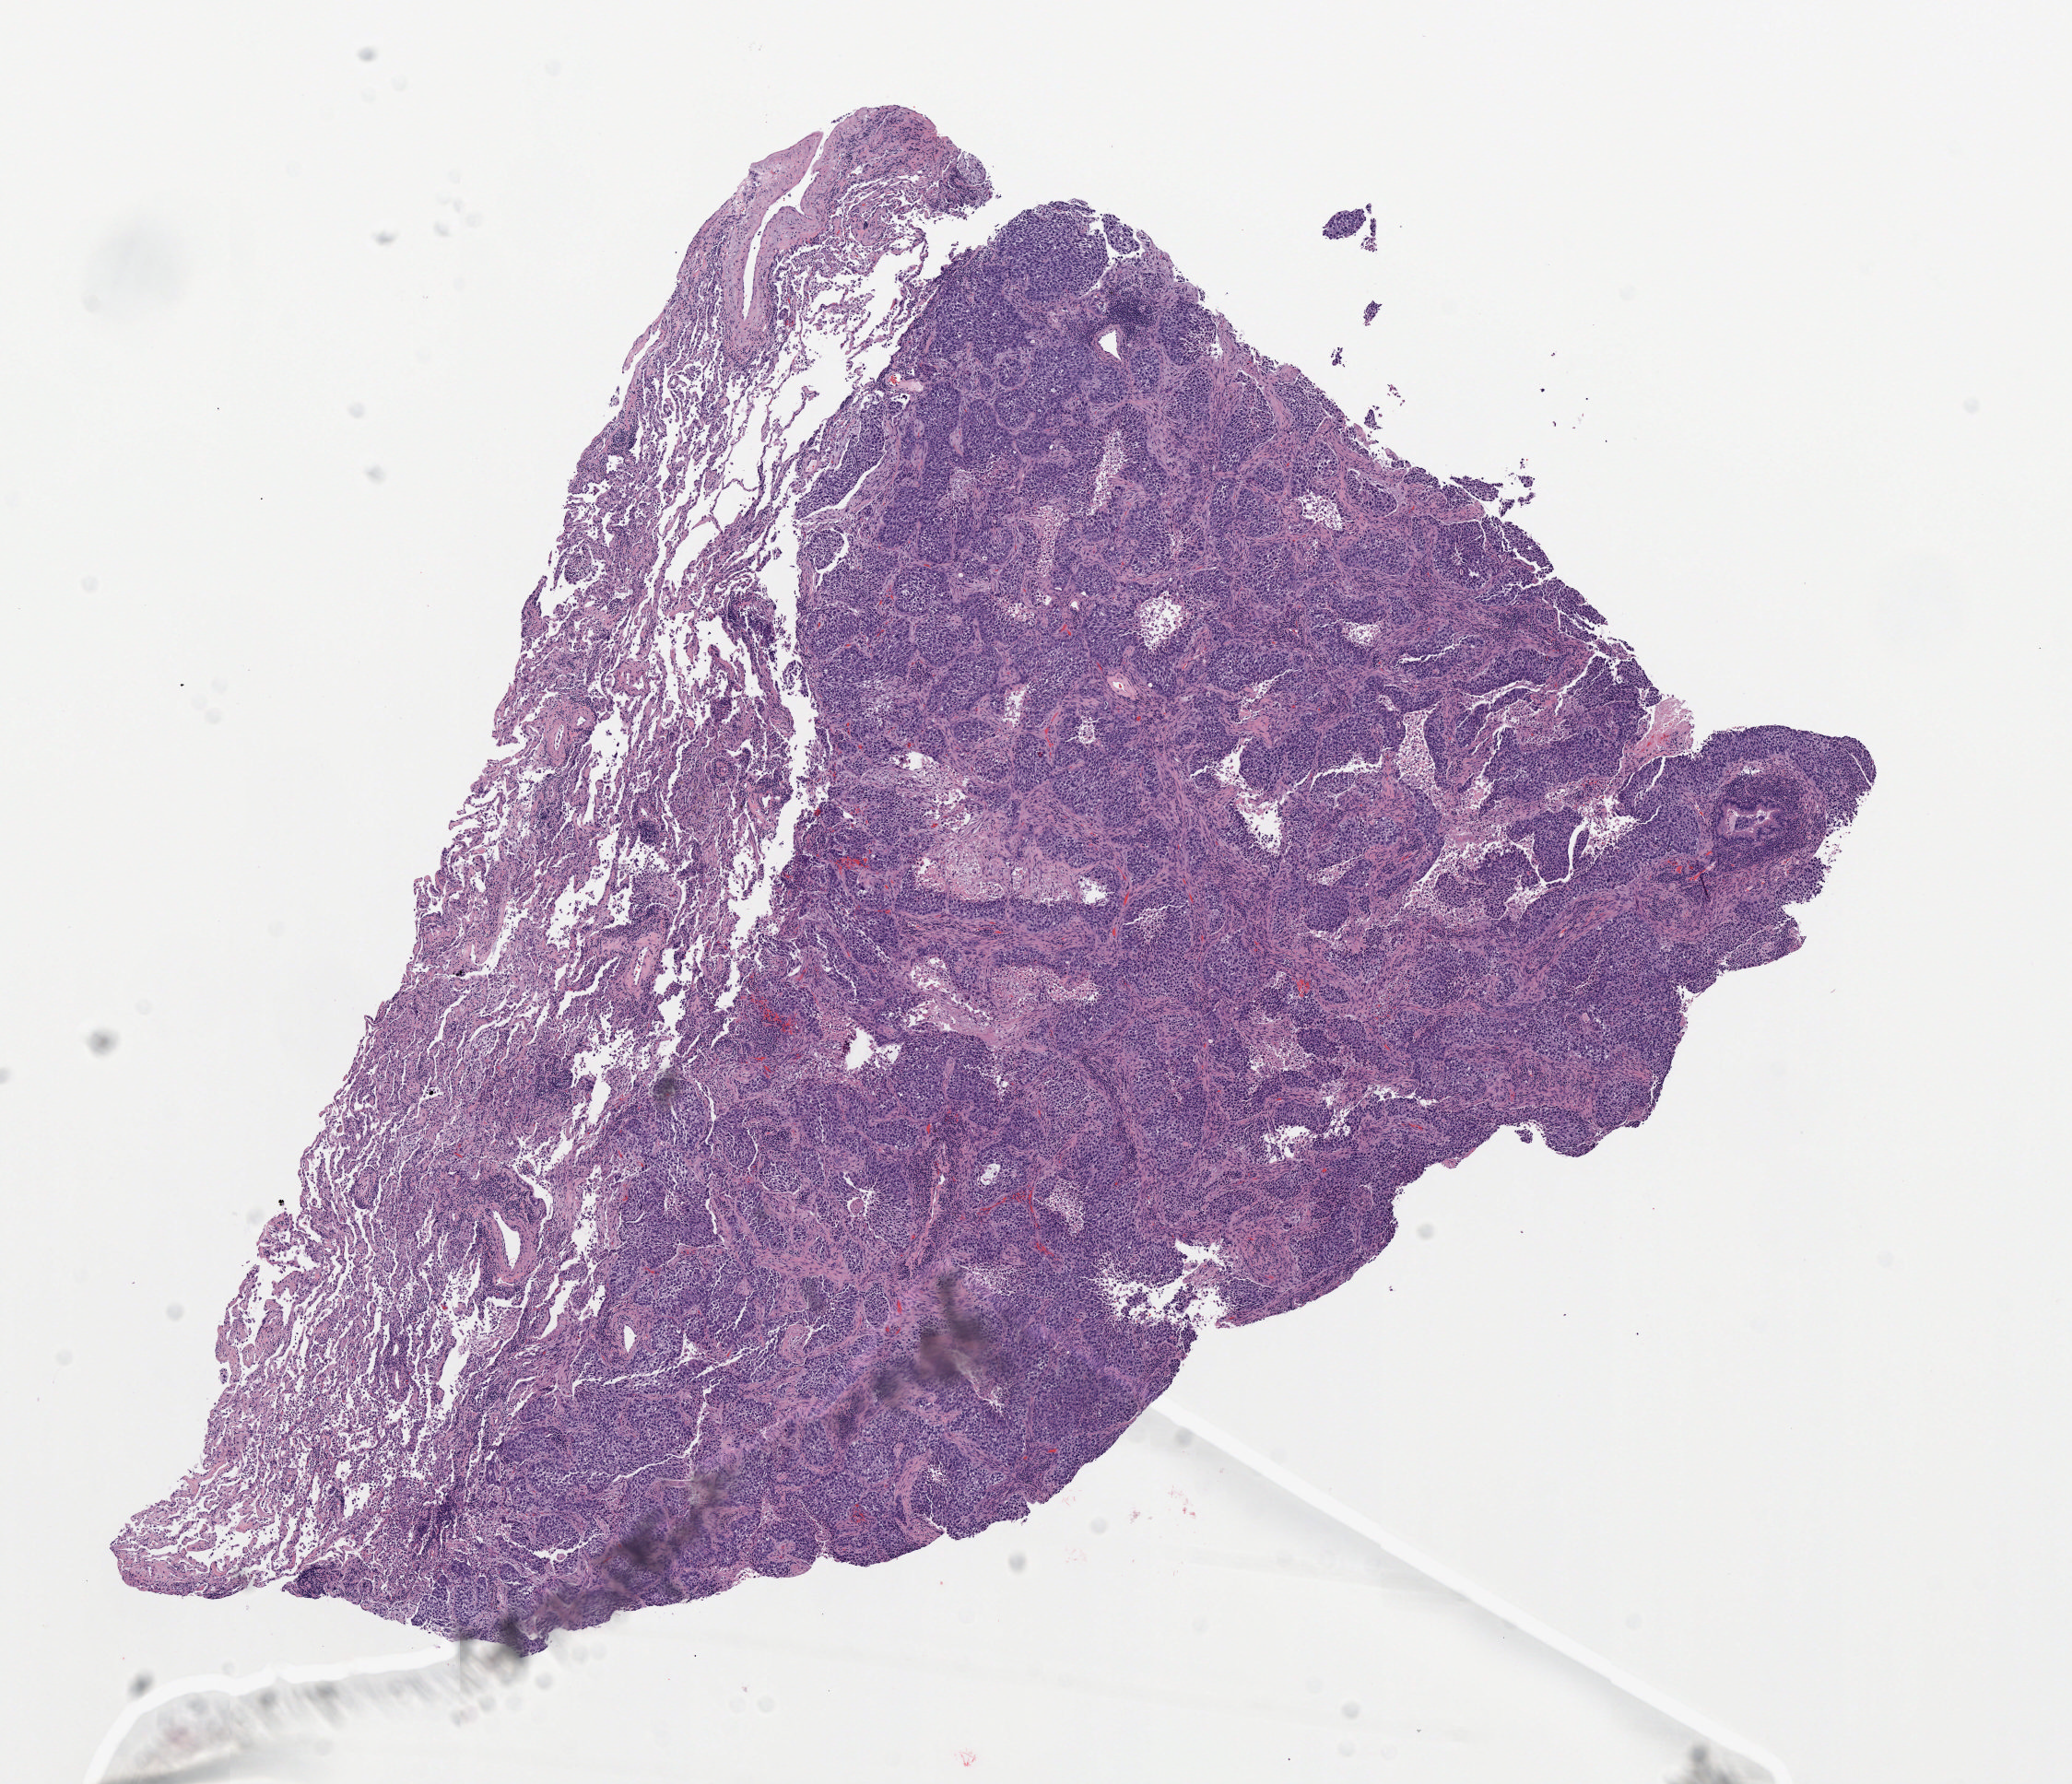
Digitized H&E tissue section (whole slide) — low-resolution overview of the scanned area, about 9.0 x 7.8 mm (acquisition: 20x scan), FFPE section, lung, primary tumour sample. Female patient.
Histologic diagnosis: Squamous cell carcinoma, NOS (lower lobe, lung).